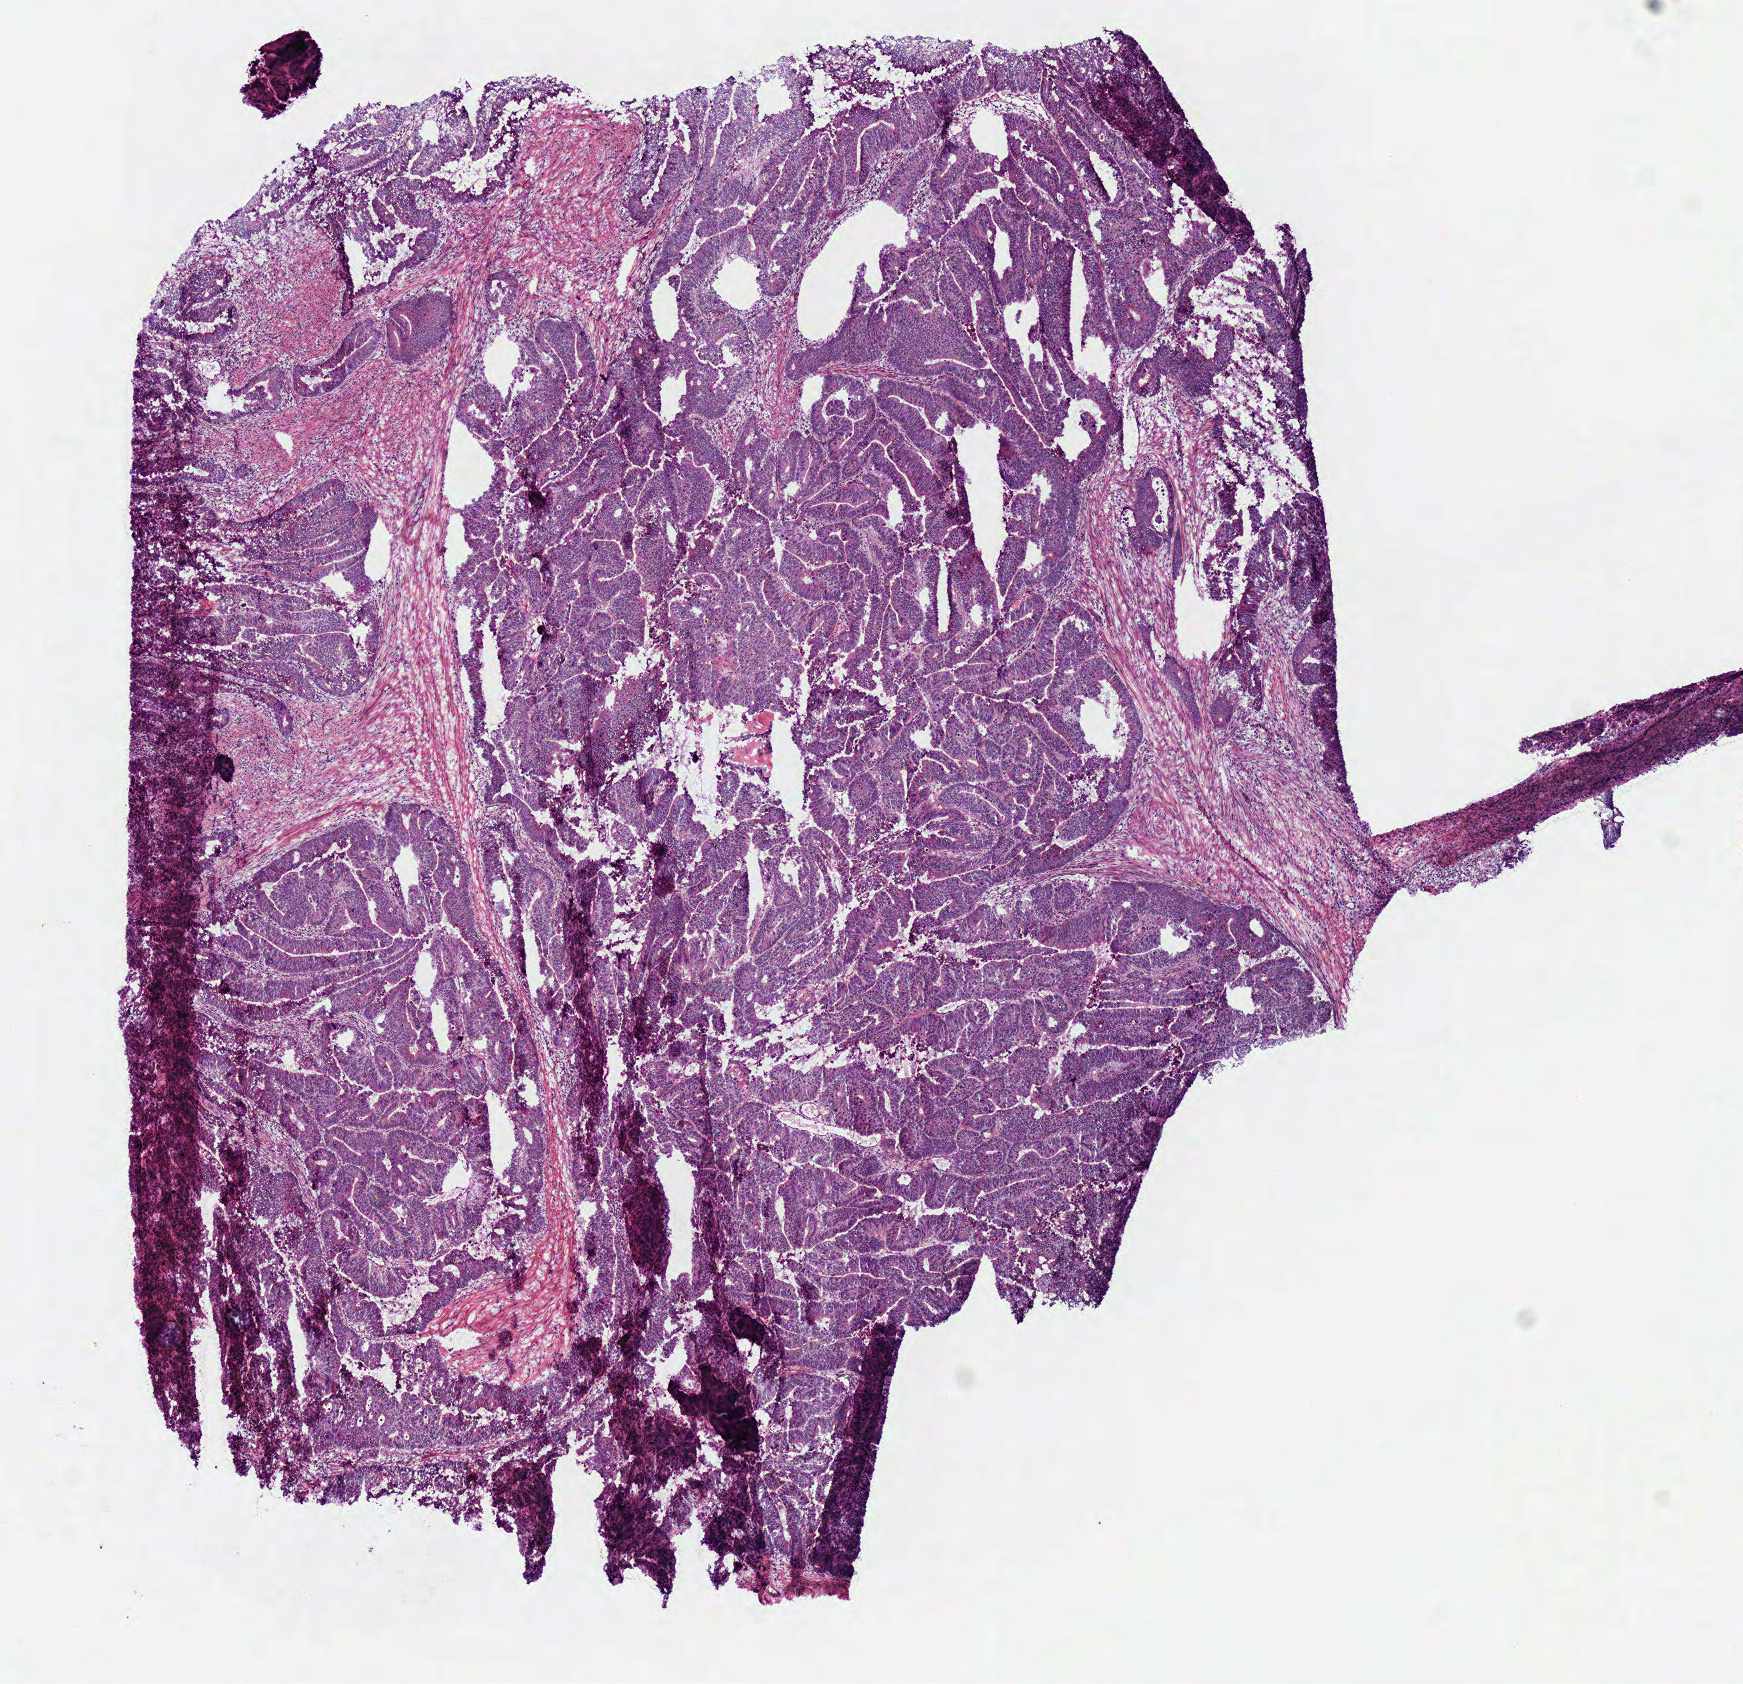
H&E-stained whole-slide image — a low-resolution overview of the entire scanned area, about 6.9 x 6.6 mm (from a 40x scan); frozen section; rectum, primary tumour sample. Male patient; age at initial diagnosis 58 years. Slide review estimates, as recorded: tumour cells 80%, tumour nuclei 80%, normal cells 0%, stromal cells 12%, necrosis 8%.
AJCC pathologic stage: IV (7th edition). Diagnosis: Tubular adenocarcinoma. Lymph nodes positive (case pathology): 7 of 13 examined.